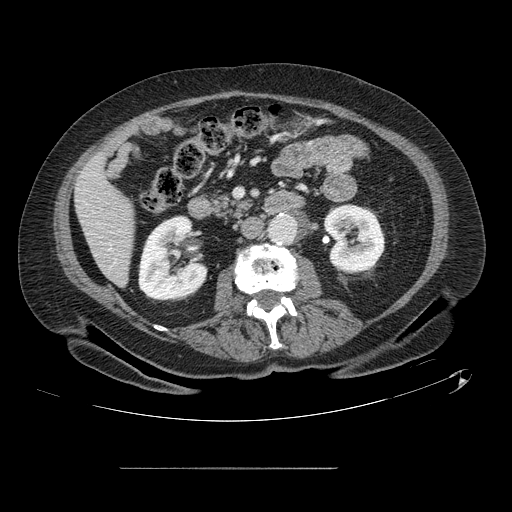
Contrast-enhanced abdominal CT, one axial slice. Position 34 of 148 along the scan axis. Intravenous contrast given. Soft-tissue window (W 400 / L 40 HU). 2.5 mm slice thickness. 512 × 512 image matrix, field of view 439 × 439 mm. Female patient, age 75 years. From the clinical record (not read from this slice): diagnosis: colorectal cancer liver metastases, imaged before liver resection; multiple liver metastases: no.
Structures marked on this image (expert manual segmentation):
- liver: box from (x=76, y=156) to (x=134, y=285) px
- planned liver remnant (the part of the liver to remain after resection): (x=76, y=156)–(x=134, y=285)